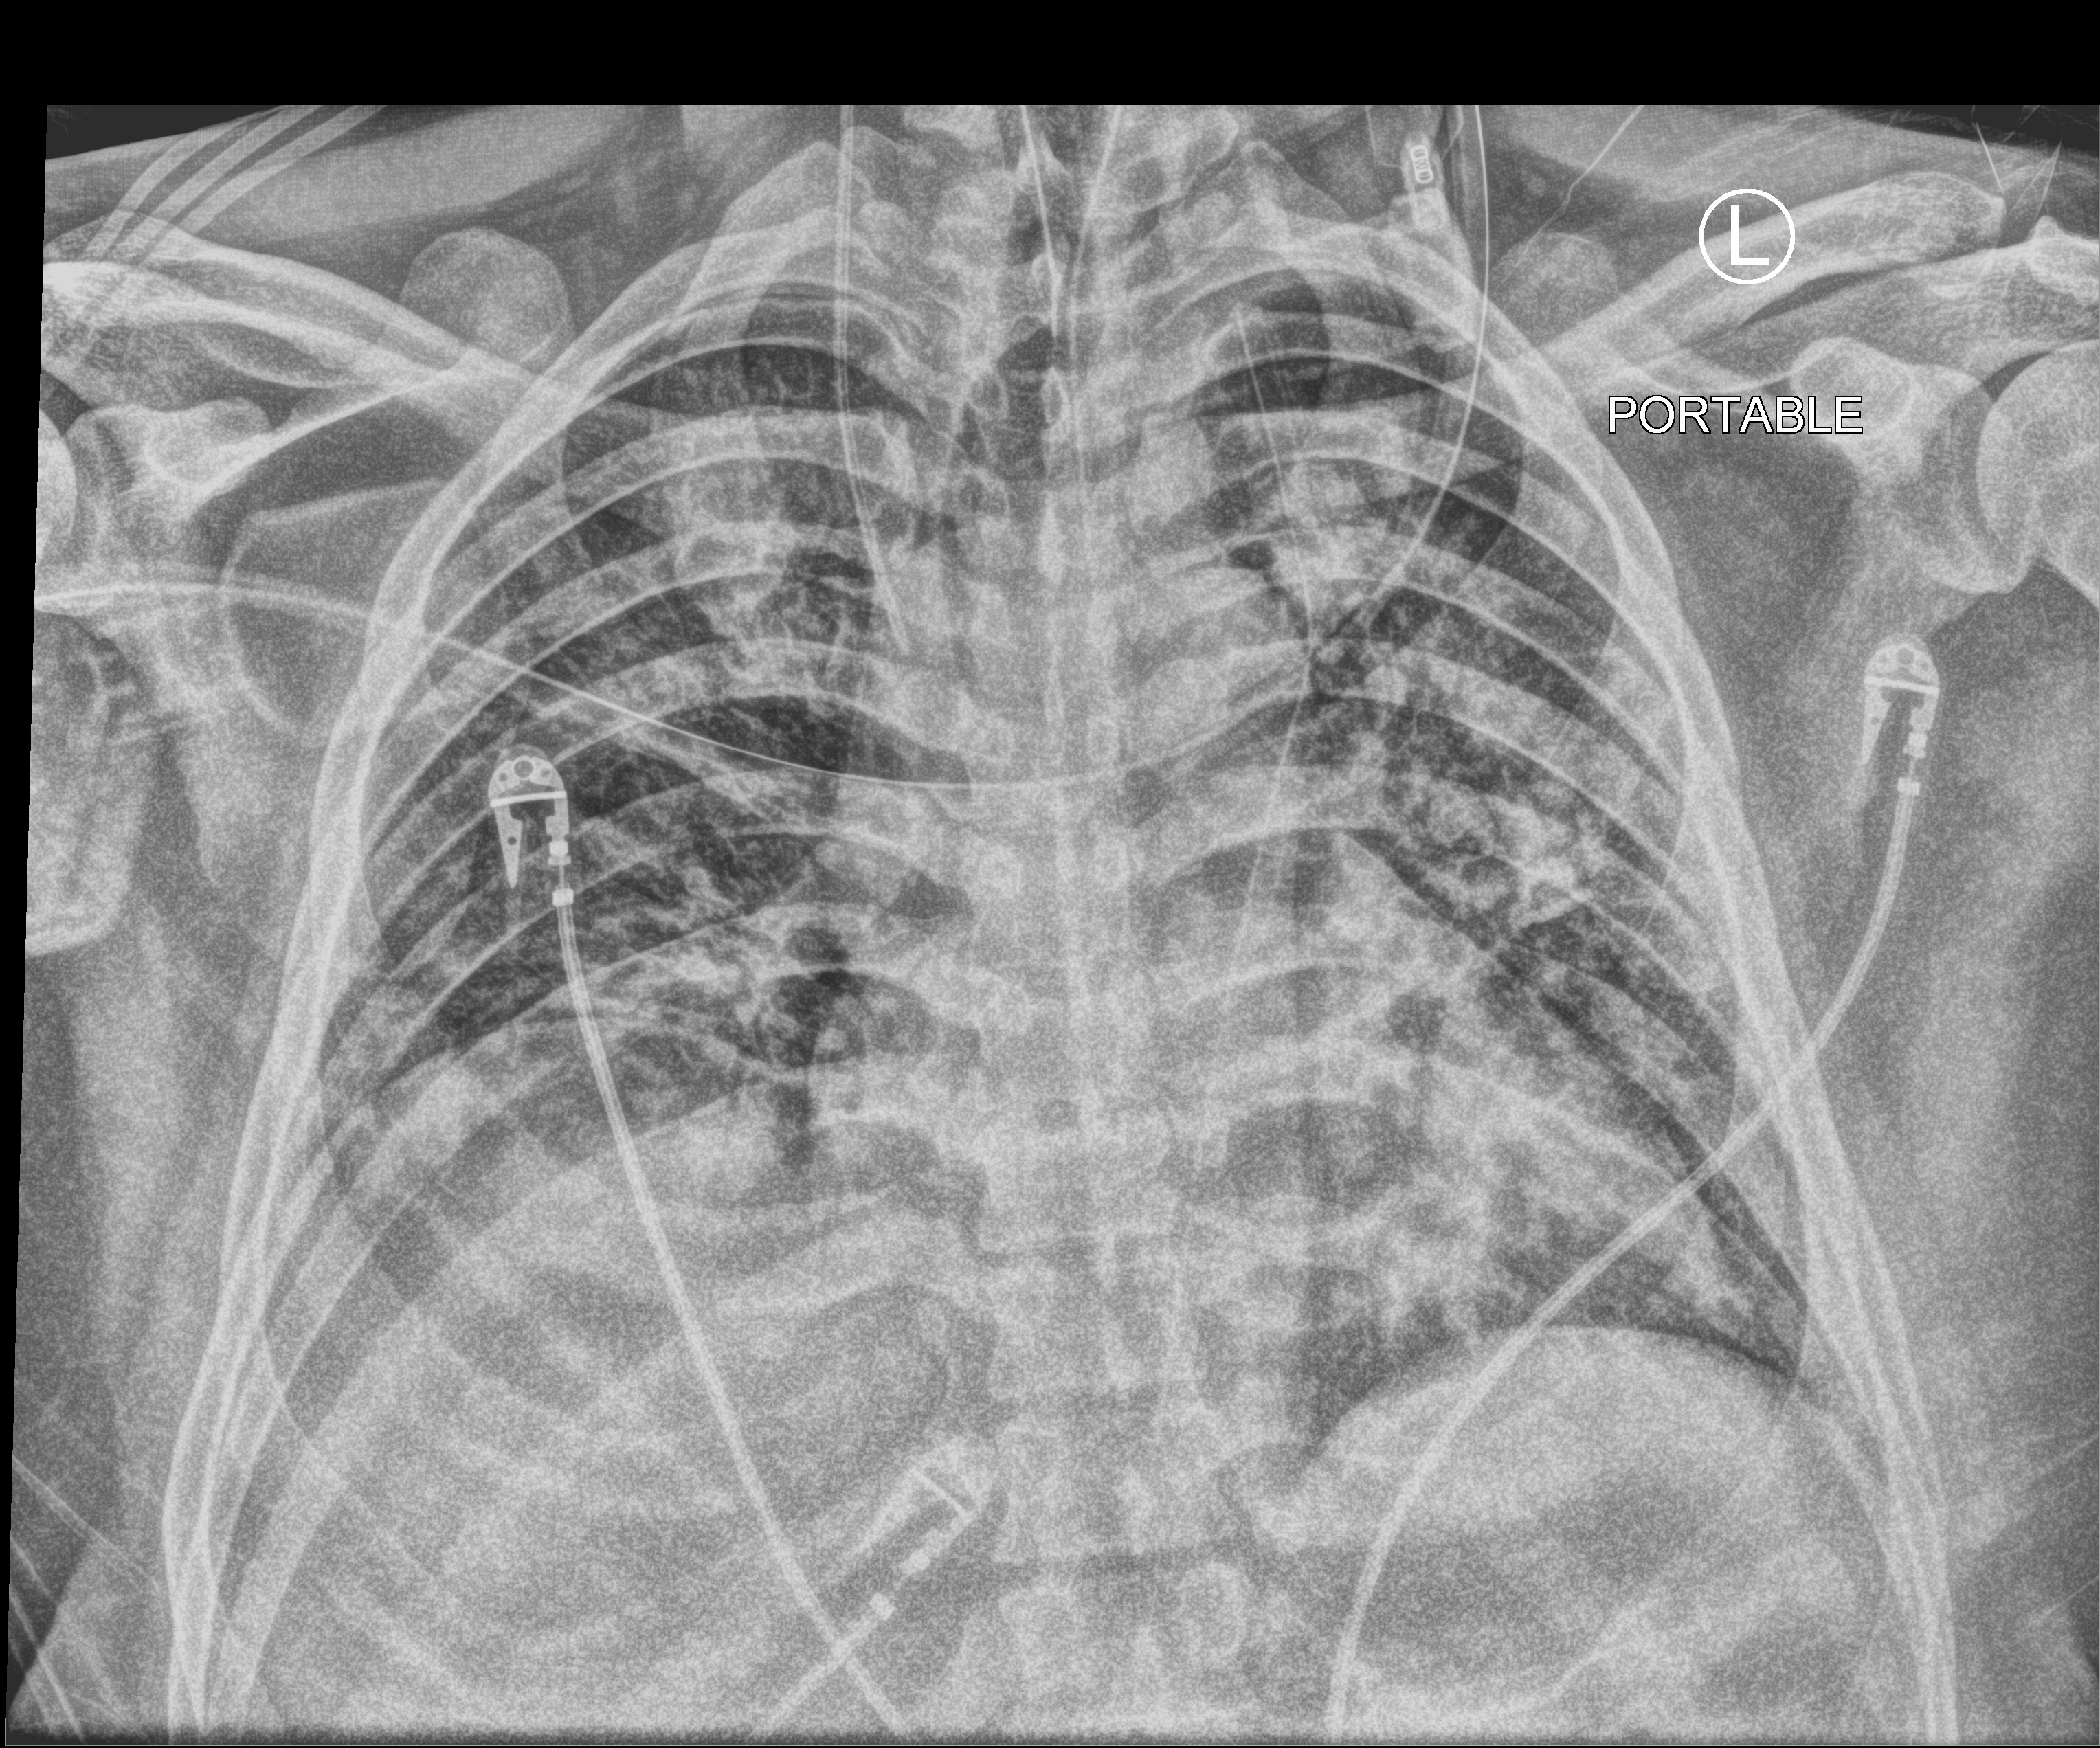
Bedside chest radiograph (computed radiography), anteroposterior (AP) projection. Male patient hospitalised with COVID-19, age 18–59 years.
From the hospital-stay record, not from the radiograph (when in the stay this image was taken is not recorded): mechanically ventilated during this hospital stay: yes; admitted to intensive care during this hospital stay: yes.